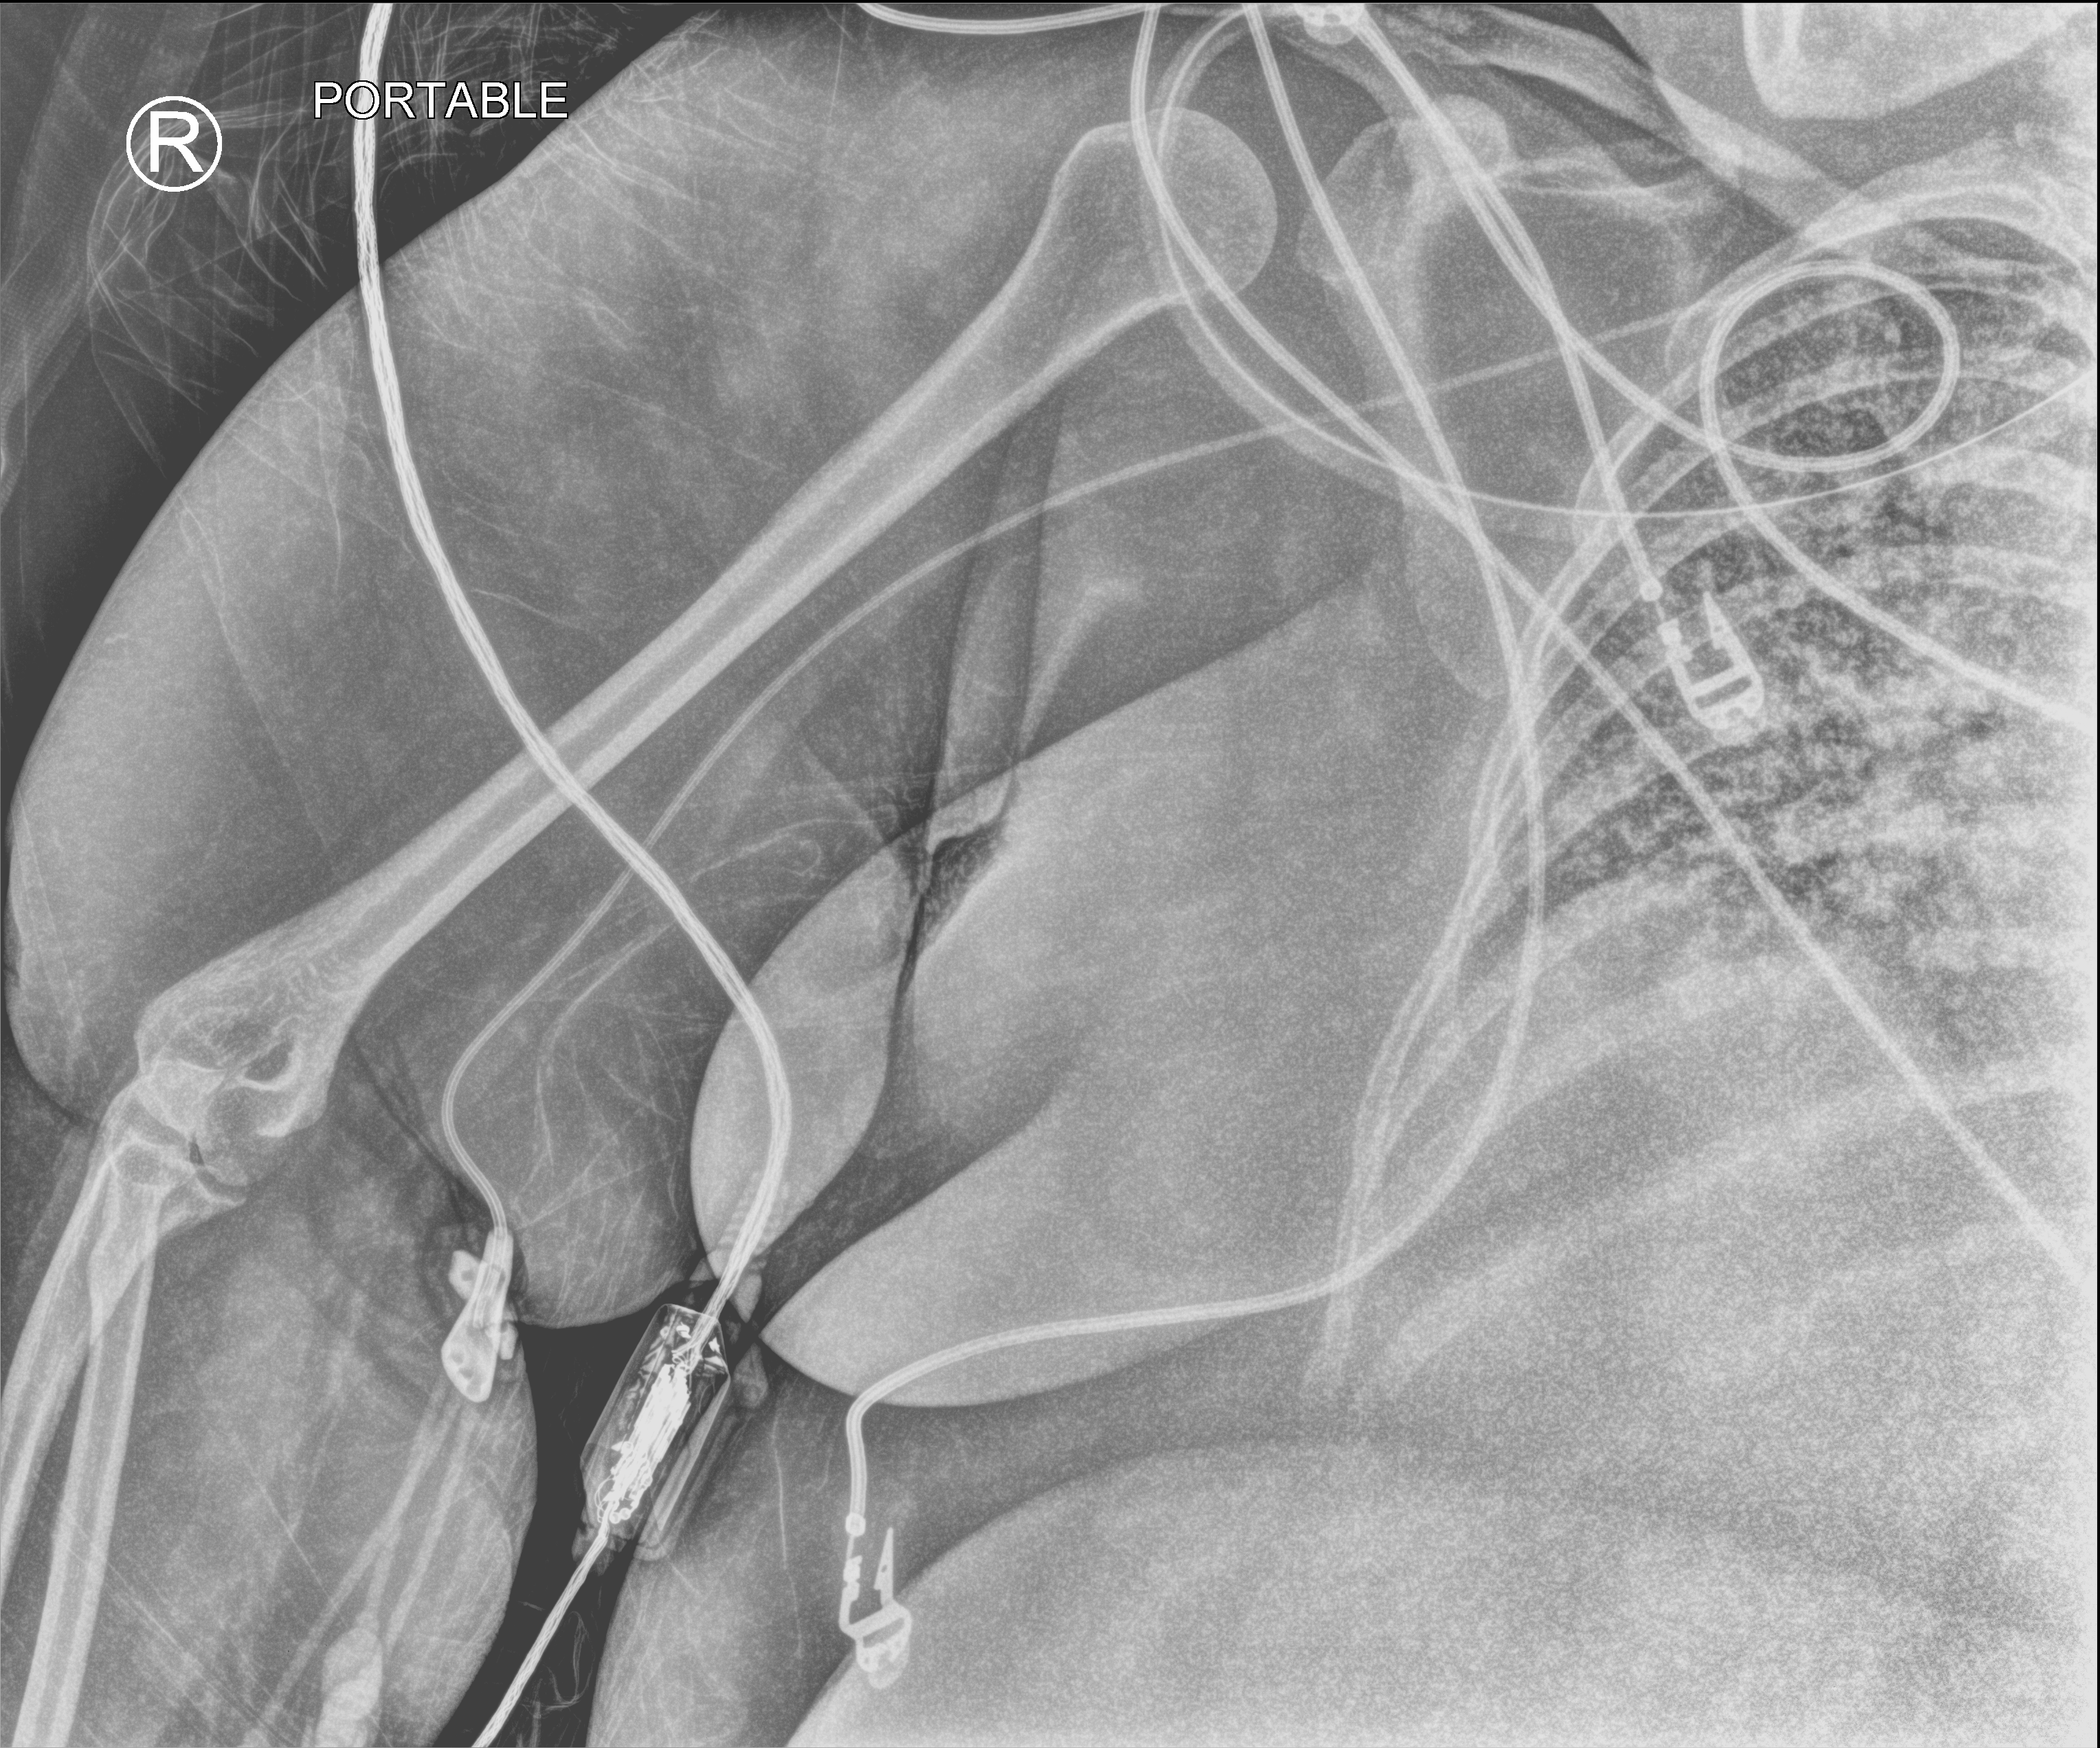
Portable chest radiograph. Female patient hospitalised with COVID-19, age 18–59 years.
Hospital-stay facts (about this admission, not read from this image; timing relative to this image not recorded): admitted to intensive care during this hospital stay: yes; hypertension (admission record): yes; length of hospital stay: 95 days.